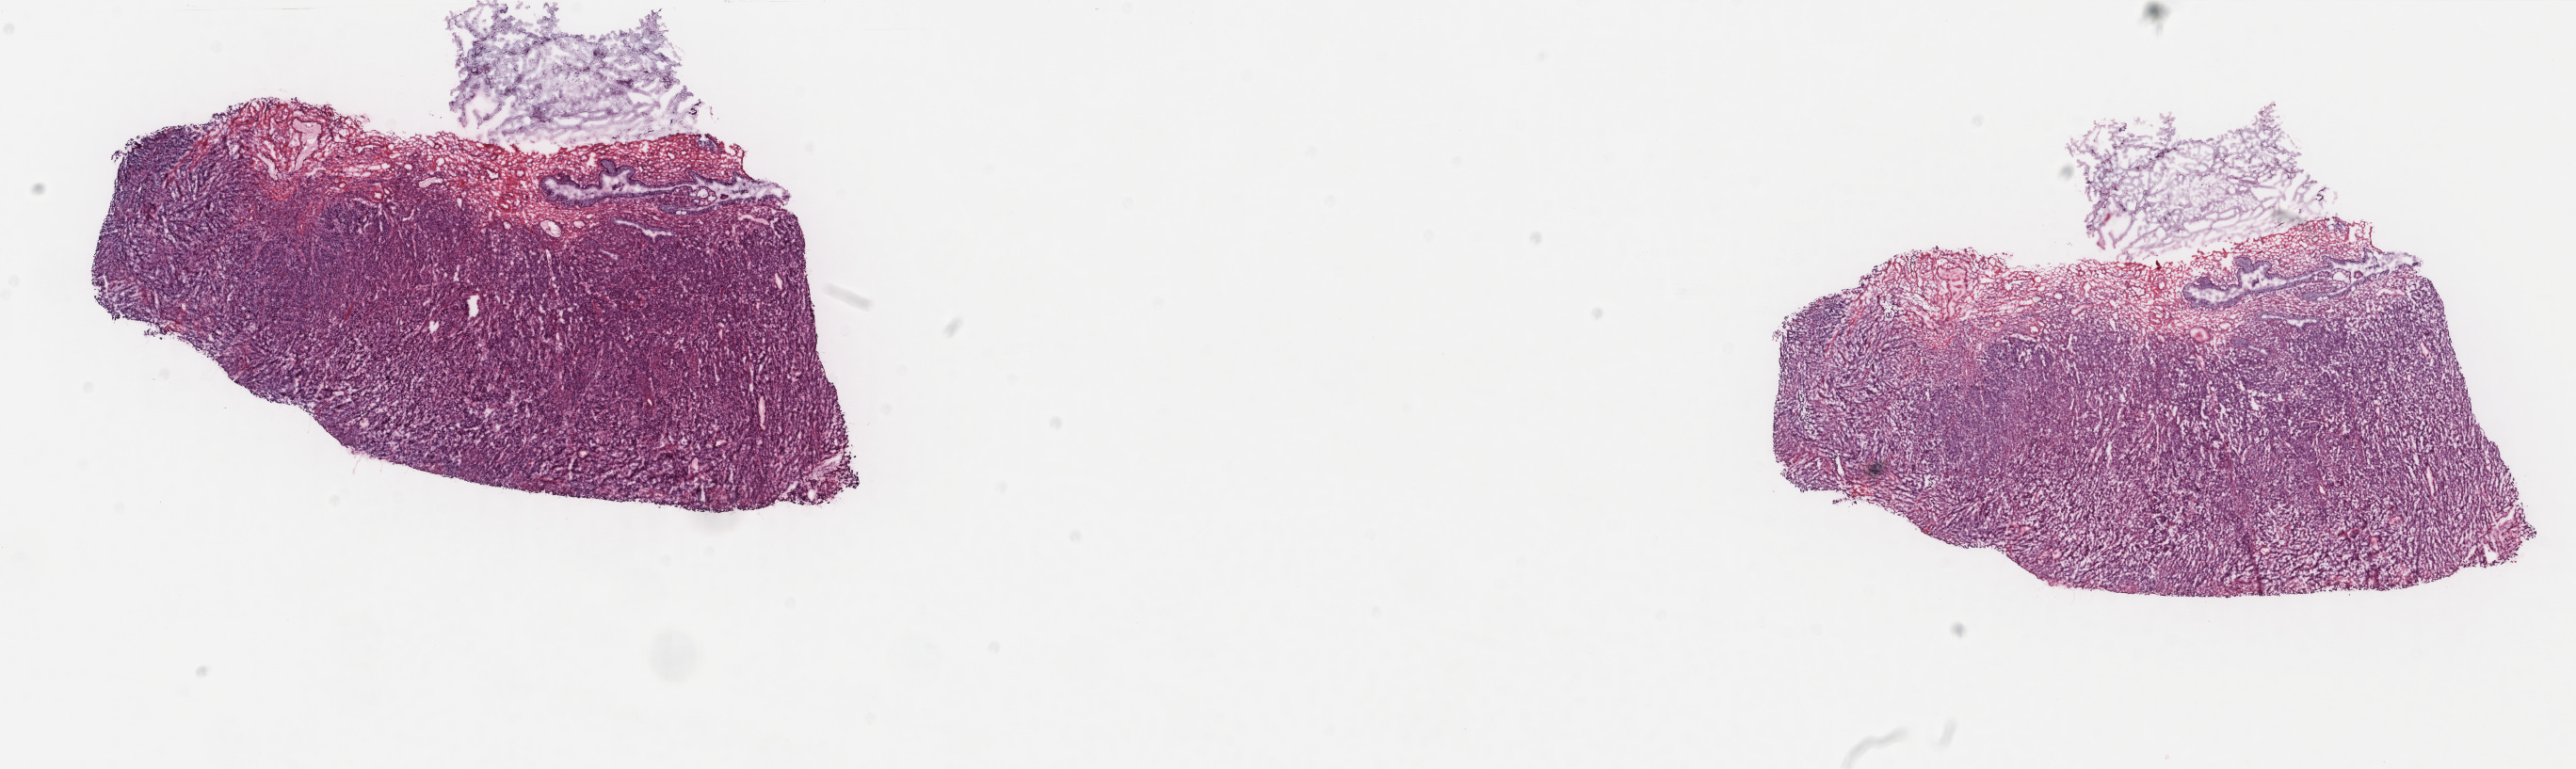
Hematoxylin and eosin (H&E) stained whole-slide image, shown as a low-resolution overview of the whole scanned area (about 21.7 x 6.5 mm, slide scanned at 40x). Frozen section. Primary tumour sample from the cervix. Female, age 45 years at initial diagnosis.
Histologic diagnosis: Squamous cell carcinoma, large cell, nonkeratinizing, NOS.